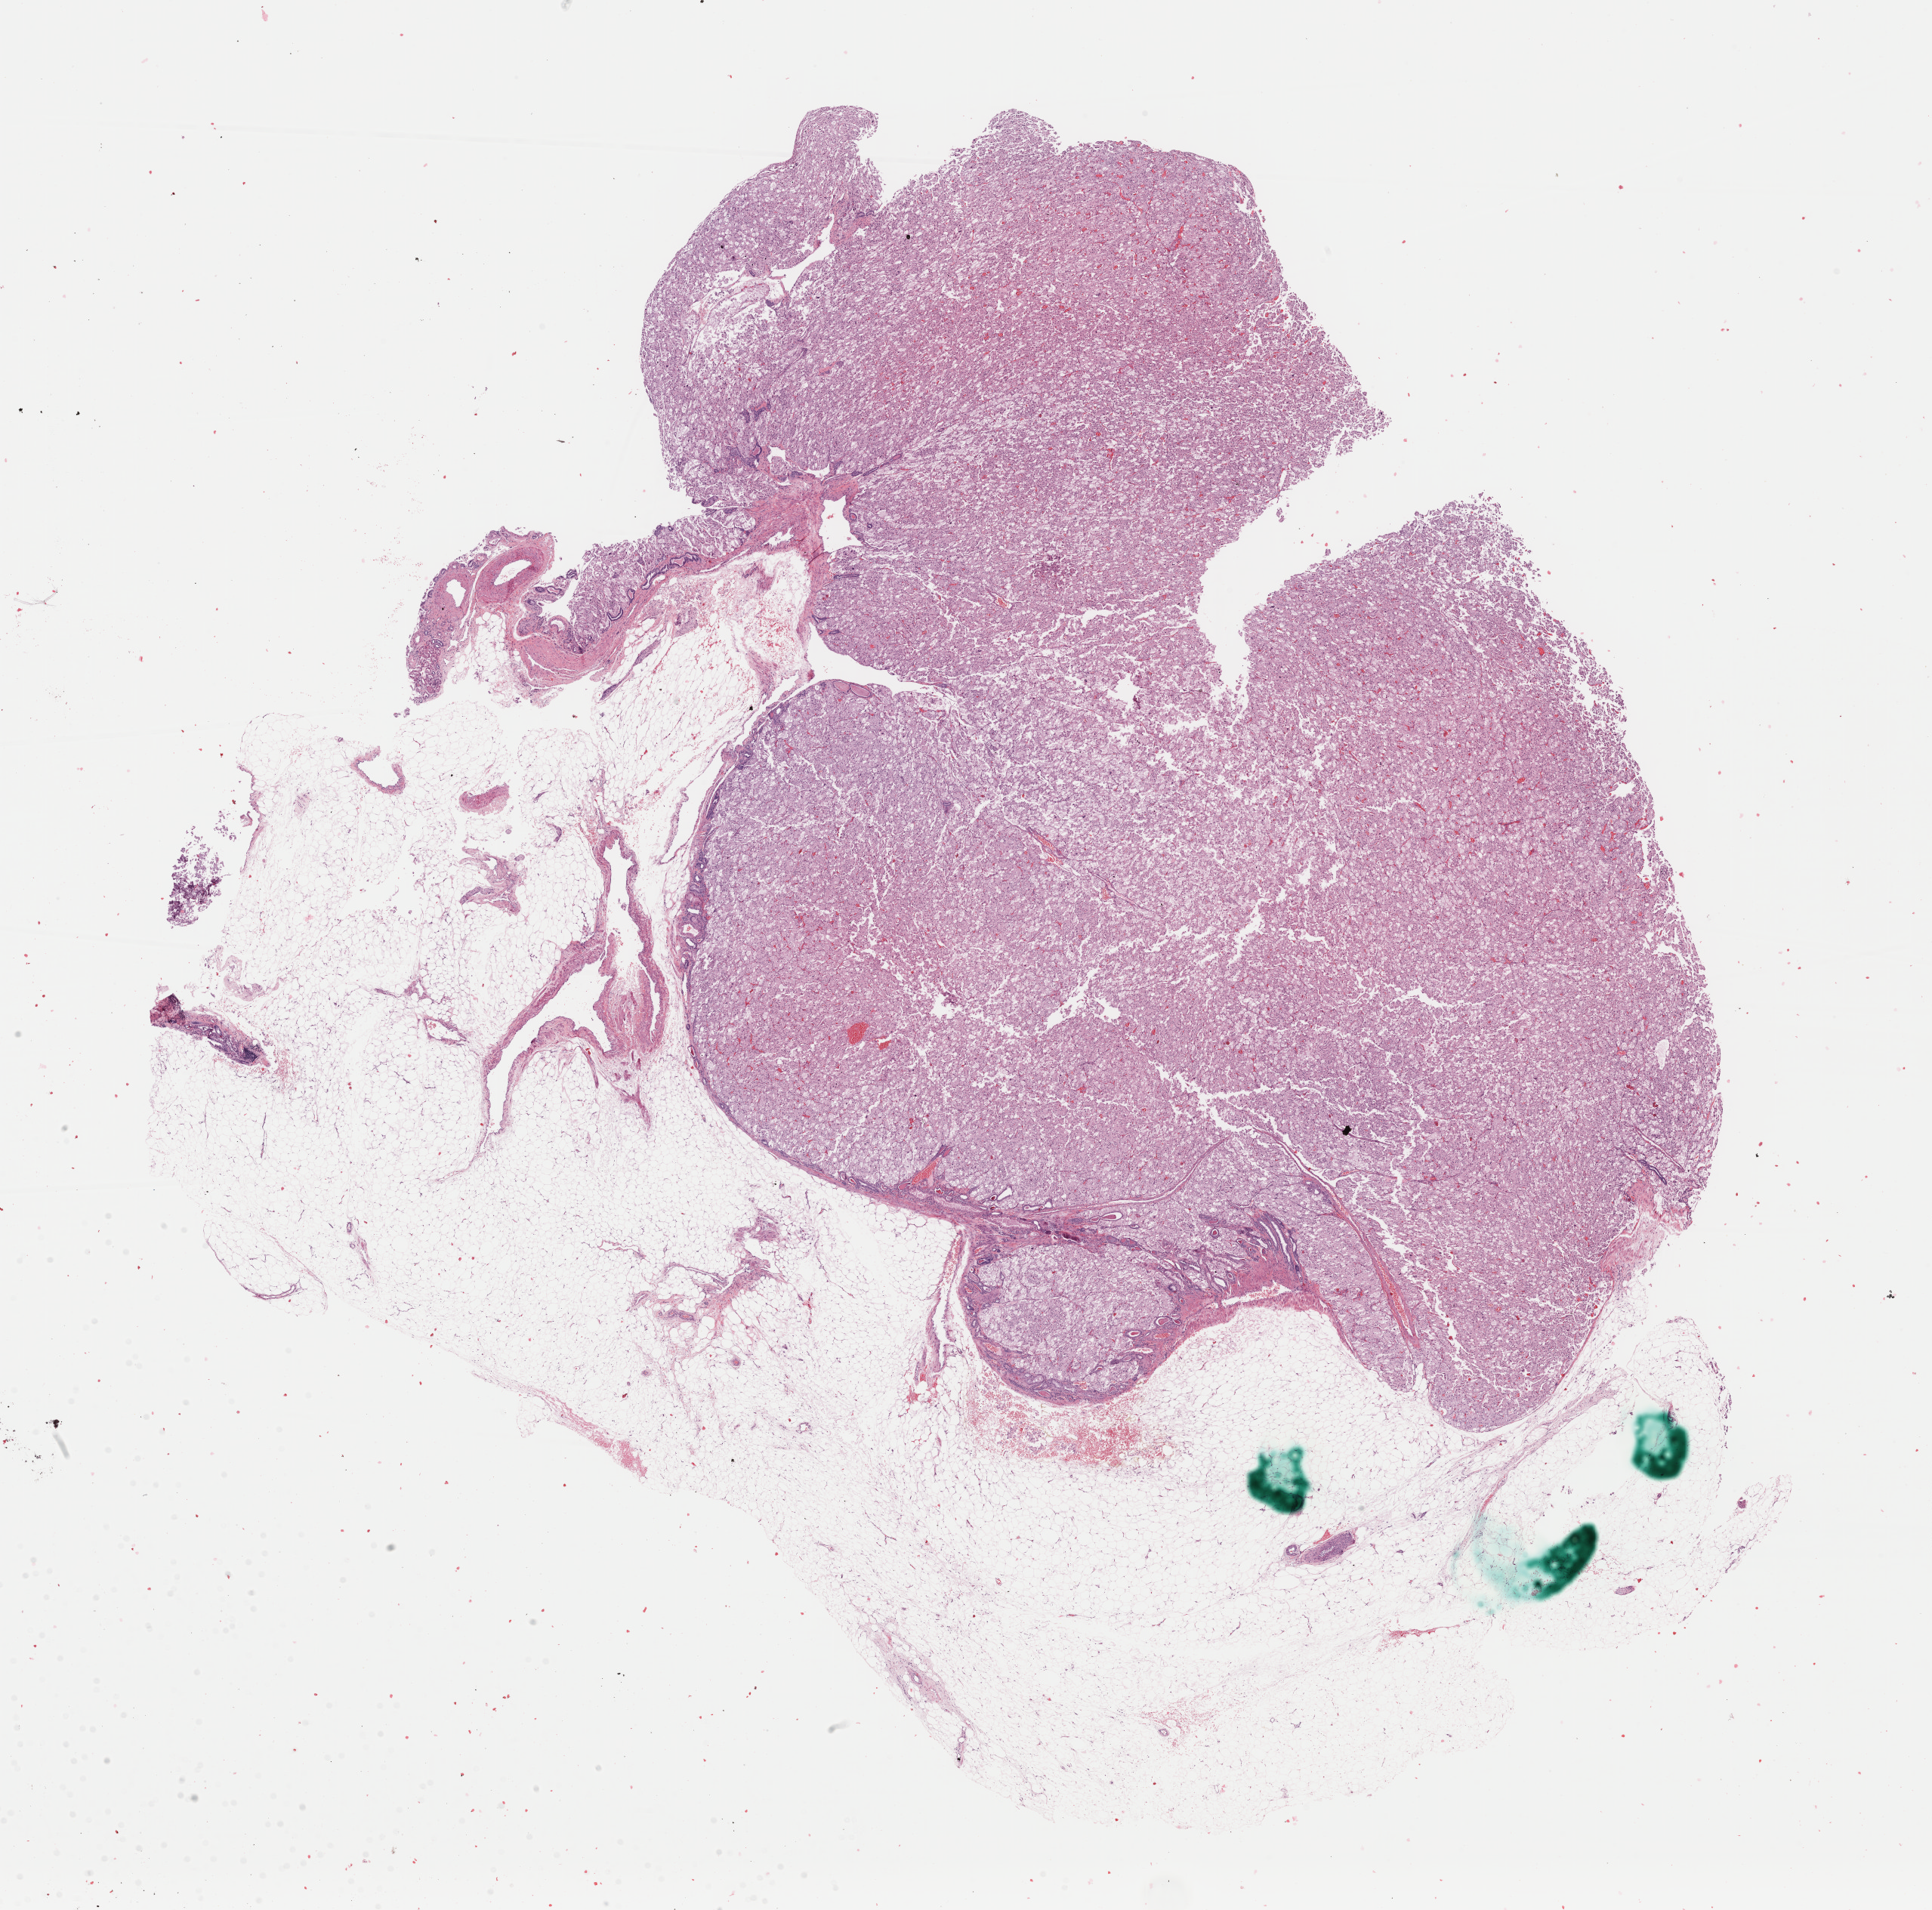
H&E whole-slide image, a low-resolution overview of the entire scanned area, about 20.2 x 20.0 mm (from a 40x scan); formalin-fixed paraffin-embedded (FFPE) diagnostic section; sample: primary tumour, kidney. Patient: male, age at initial diagnosis 58 years.
Diagnosis: Renal cell carcinoma, chromophobe type. AJCC pathologic stage: I.